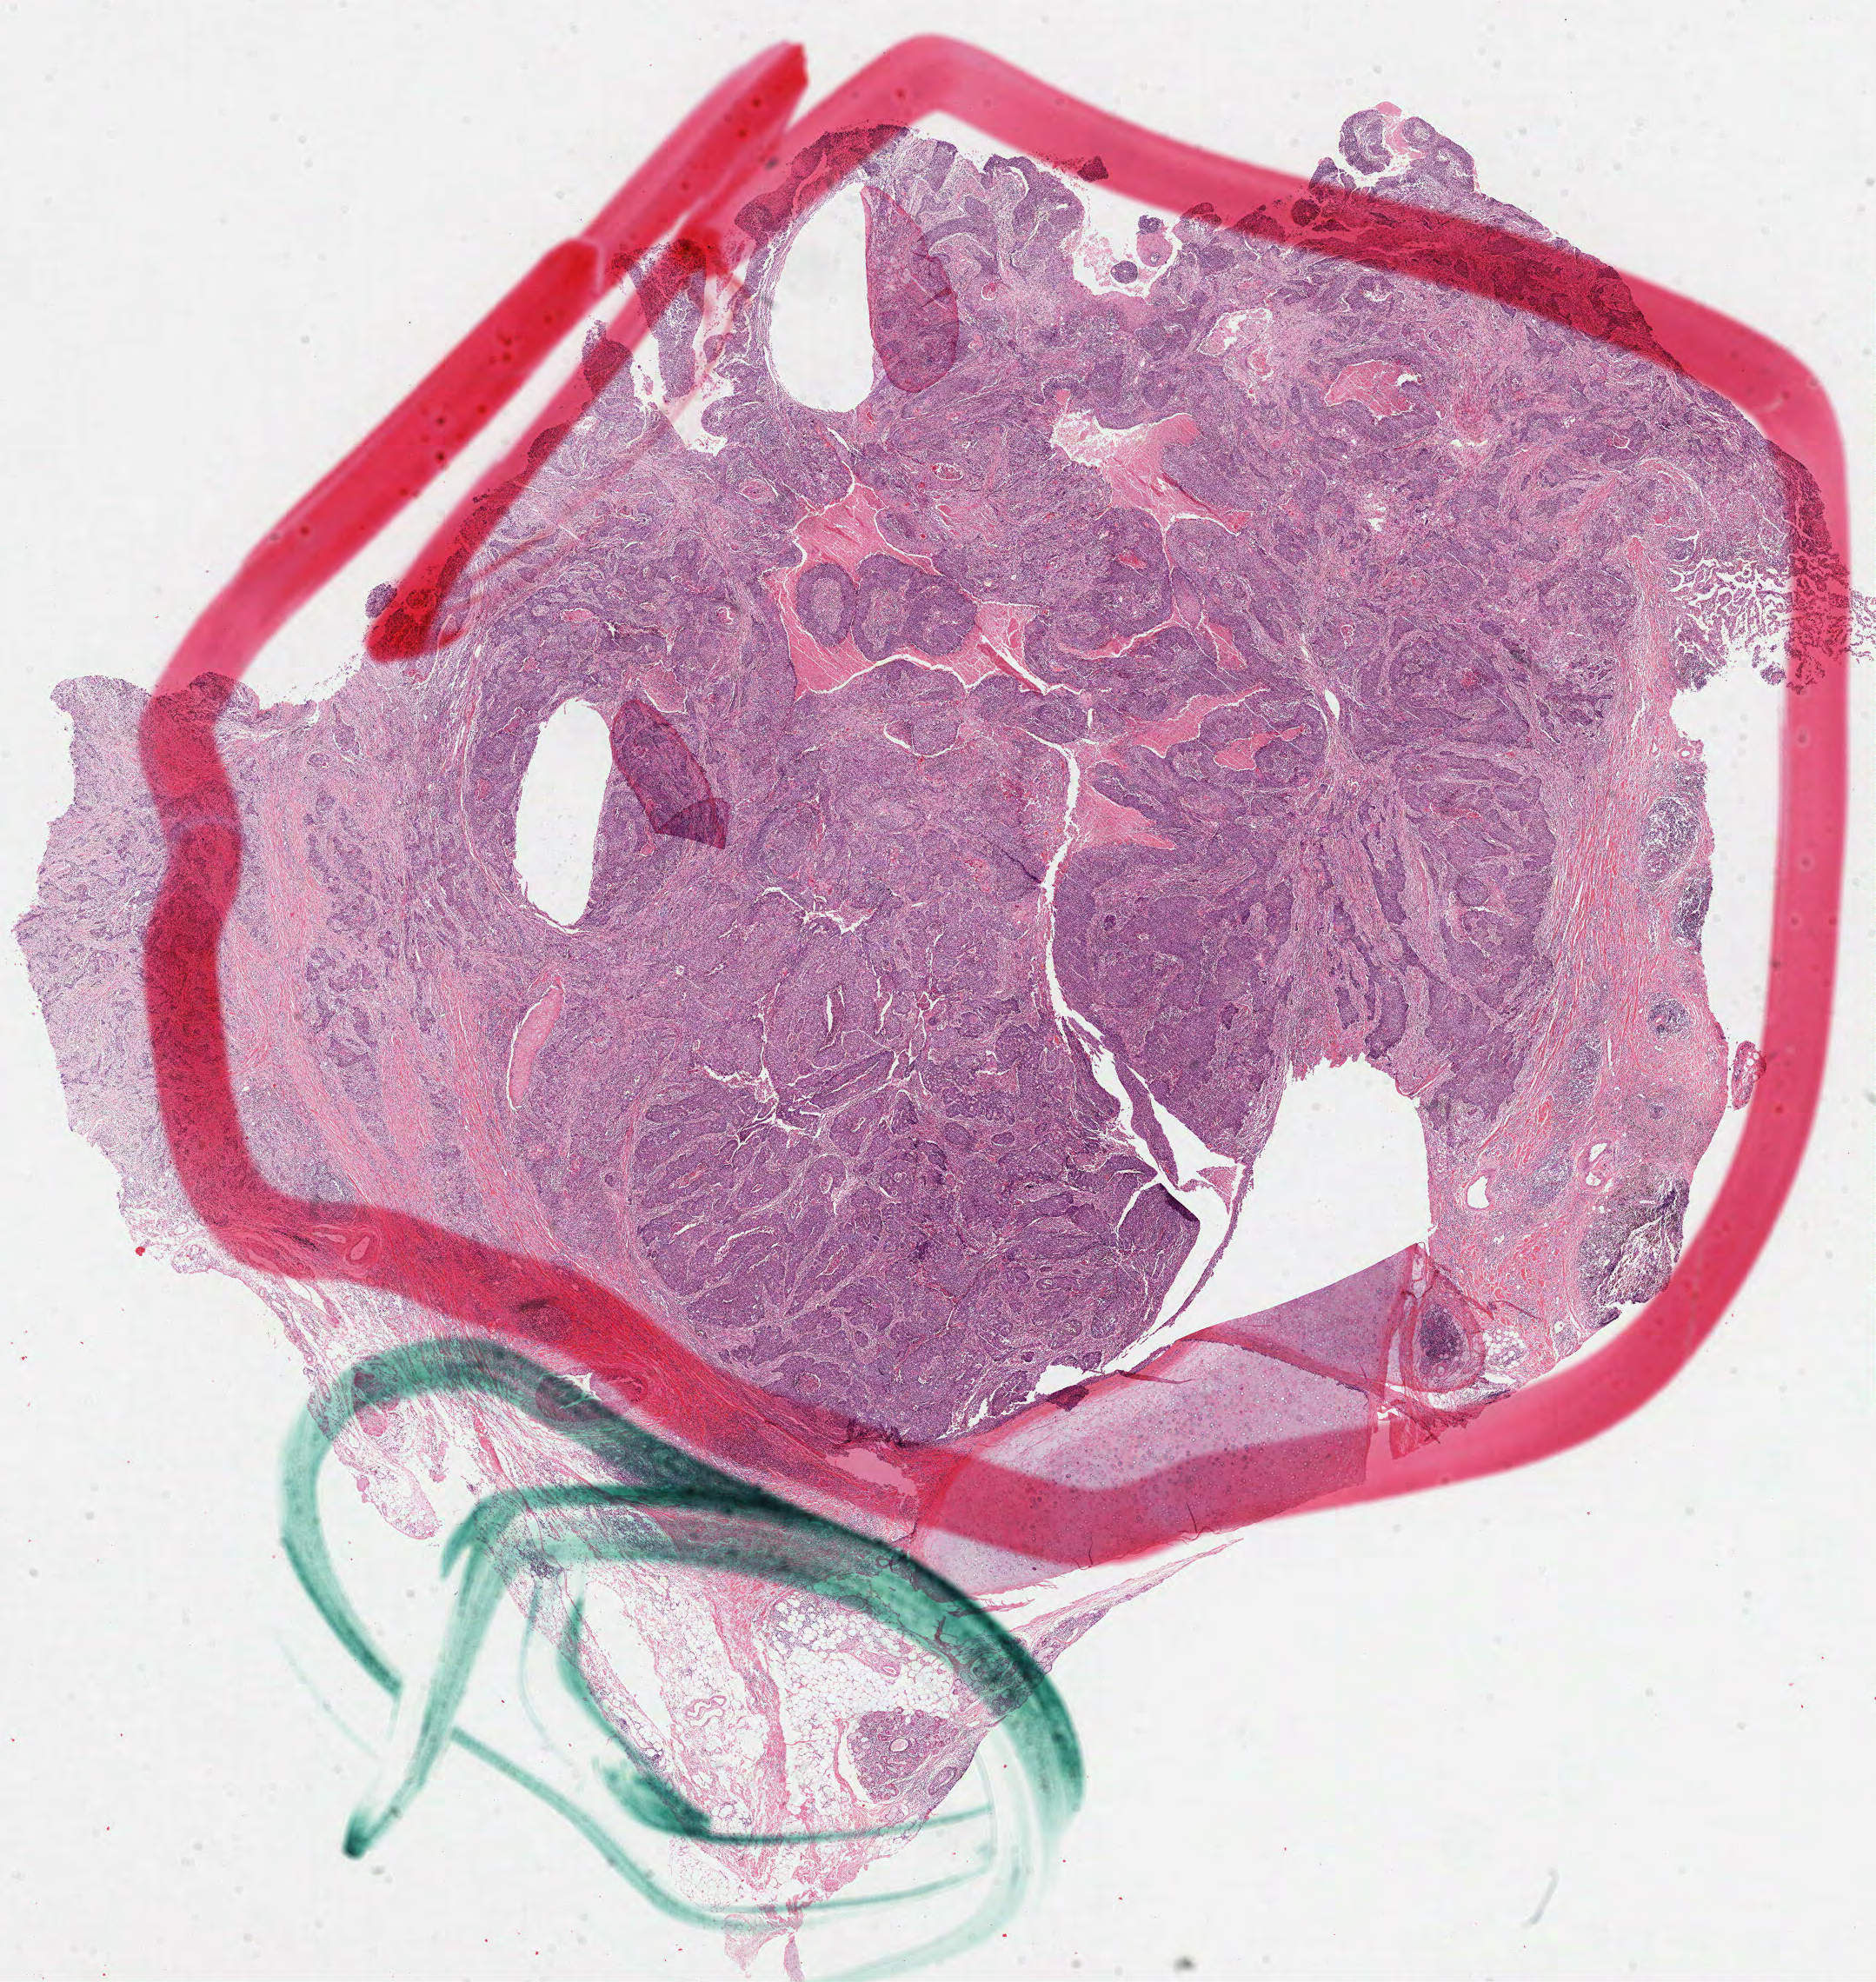
Digitized Hematoxylin and eosin (H&E) stained tissue section (whole slide) — a low-resolution overview of the entire scanned area, about 17.4 x 18.4 mm (acquisition: 40x scan); FFPE section; lung, primary tumour sample. Patient: male, age at initial diagnosis 73 years.
* AJCC pathologic stage: IIIA (7th edition)
* TNM: T4 N0 M0
* histologic diagnosis: Squamous cell carcinoma, NOS (upper lobe, lung)